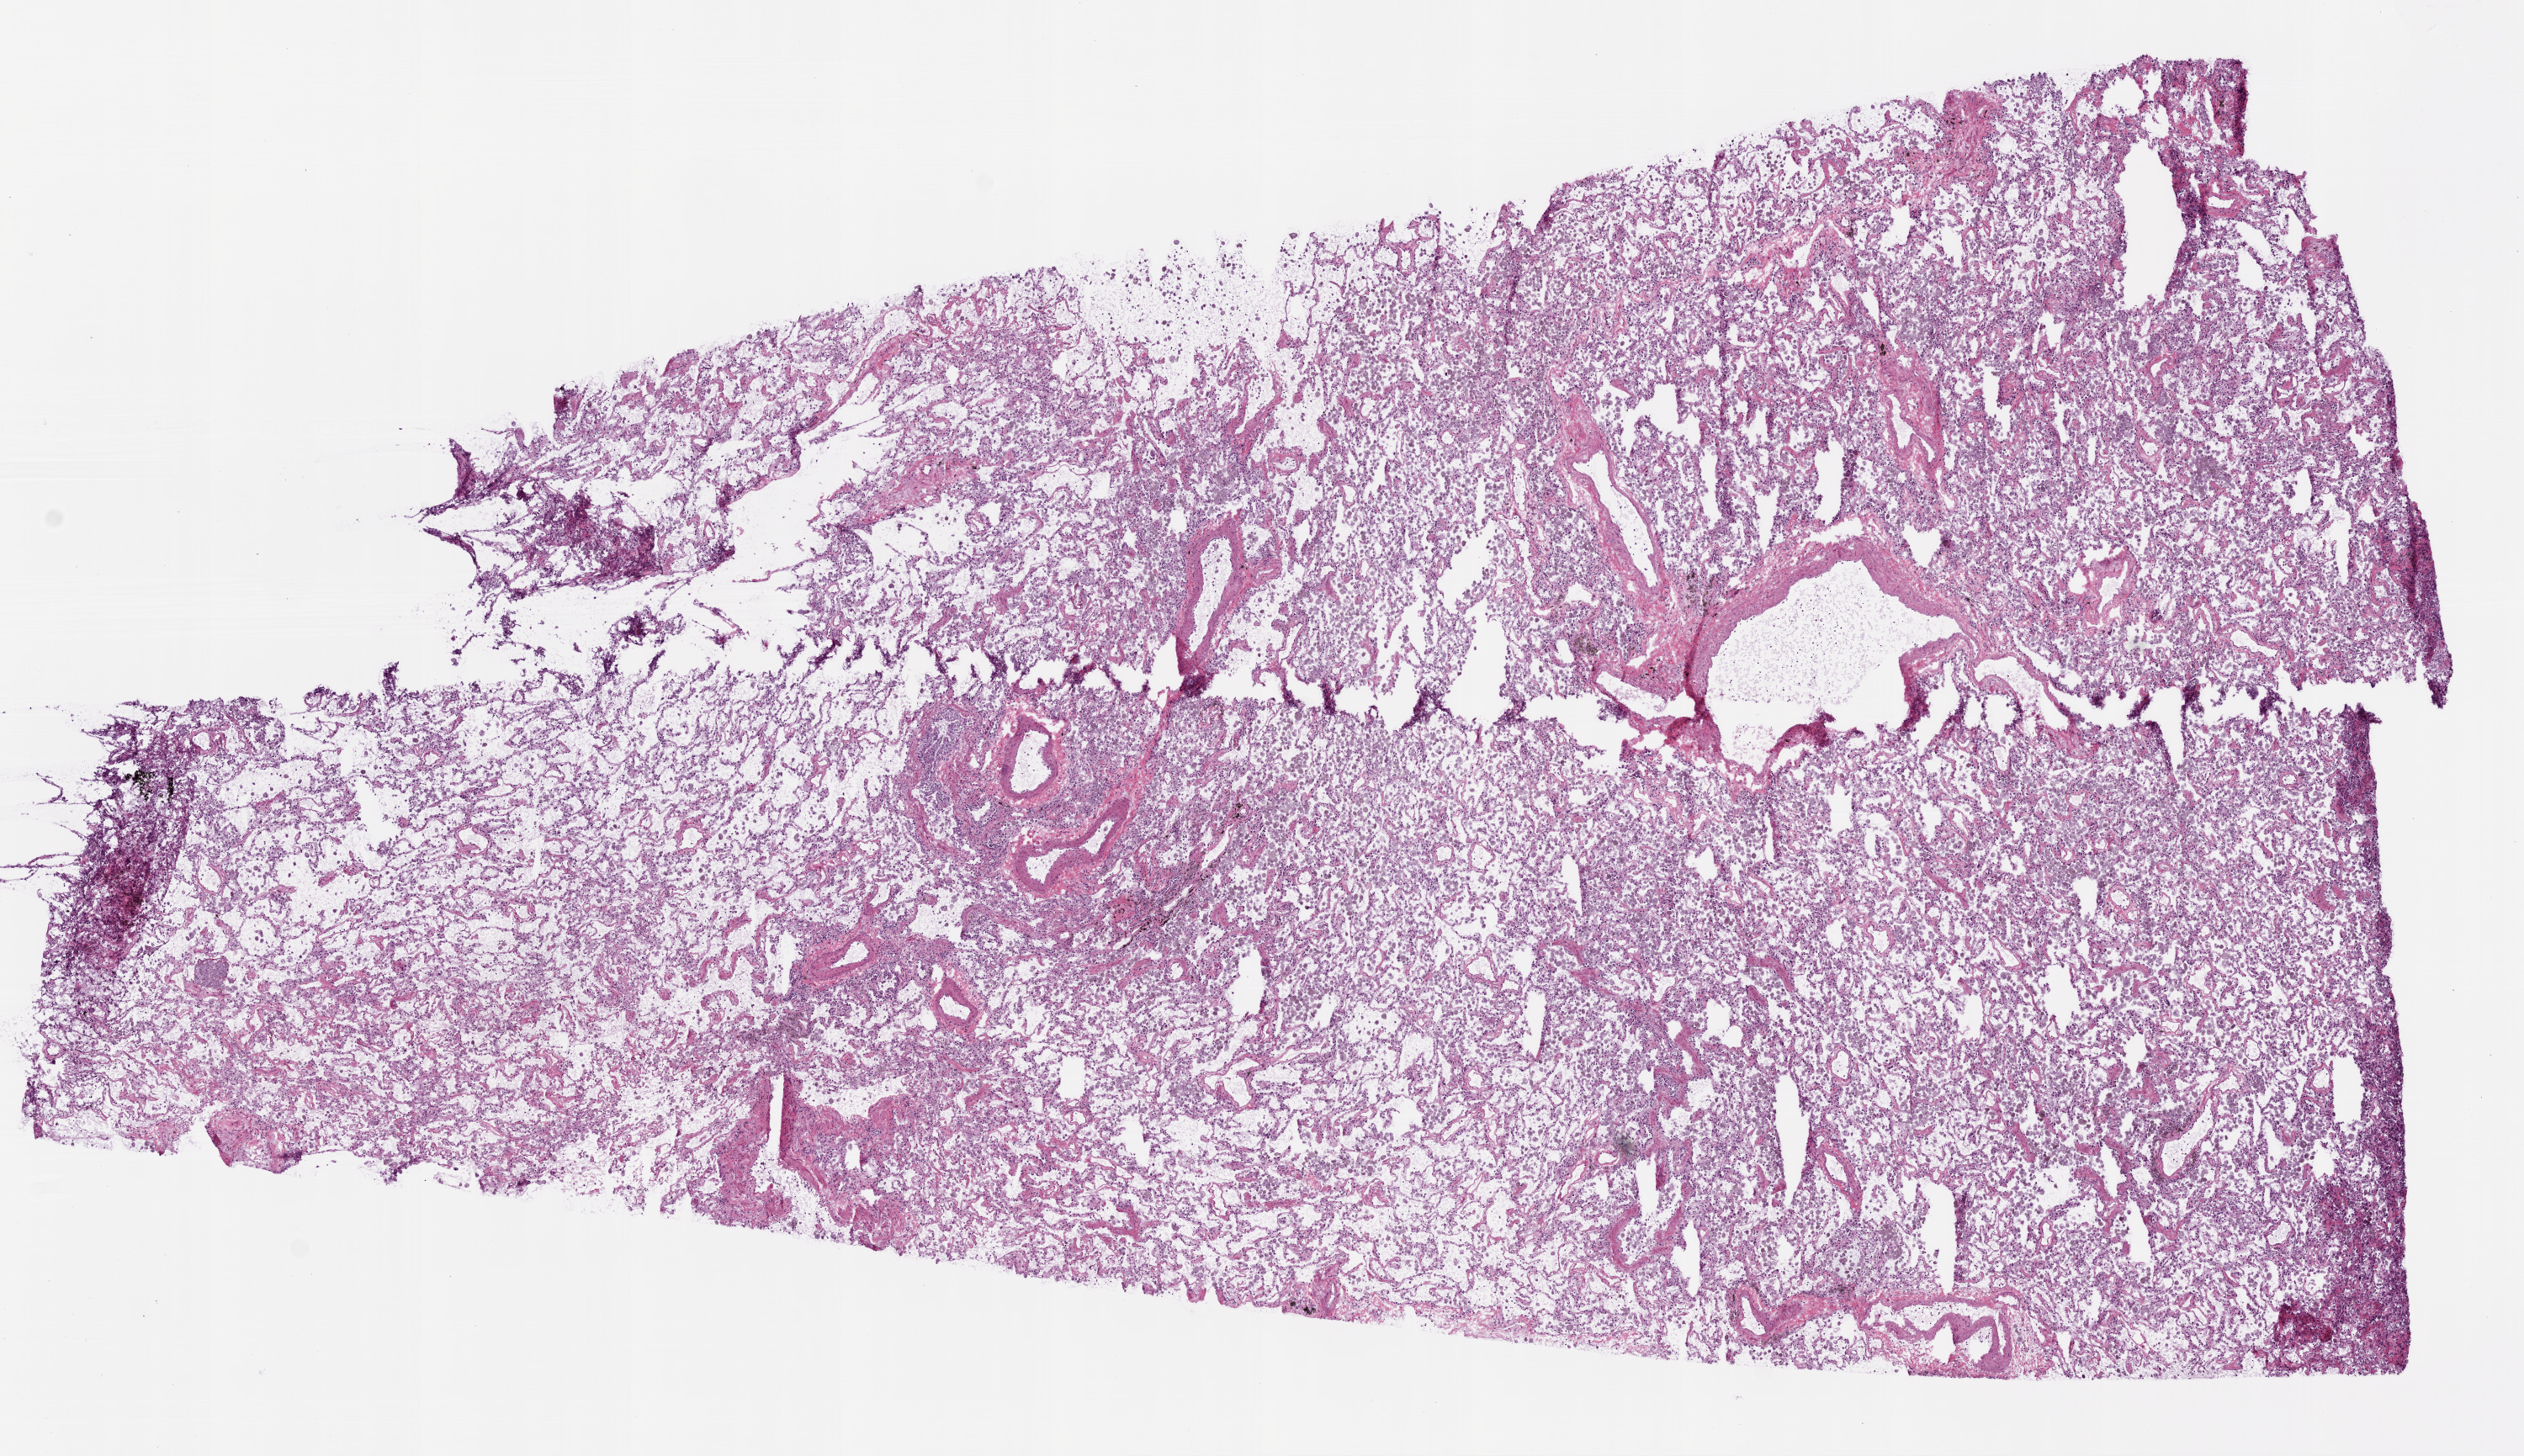
Whole-slide histology image, H&E, shown as a low-resolution overview of the whole scanned area (about 12.0 x 6.9 mm, acquisition: 20x scan), frozen section, solid tissue normal (non-tumour tissue) sample from the lung. Female patient; age at initial diagnosis 51 years.
This section: solid tissue normal sample (biorepository sample class). Patient diagnosis: Adenocarcinoma, NOS (lower lobe, lung).